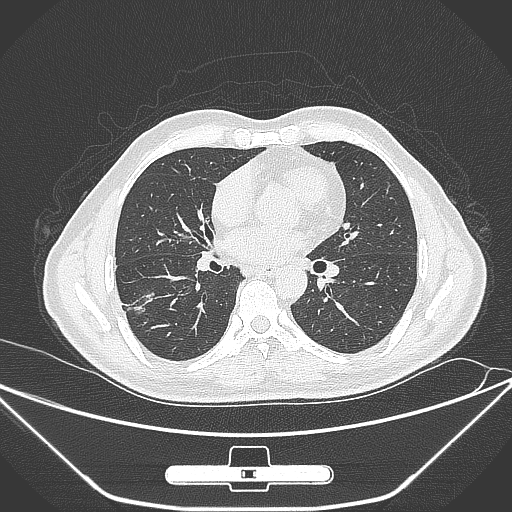
Chest CT, one axial slice. Slice 140 of 310 in the series (ordered by position). 120 kVp. Lung window (W 1500 / L -600 HU). 1 mm slice thickness. 512 × 512 image matrix, field of view 398 × 398 mm. Patient: male, 71 years. From the clinical record (not read from this slice): clinical TNM (as recorded): T1c N0 M0; histopathological grade: G2.
Outlined on this slice (bounding box drawn by a radiologist):
- lung tumour (recorded histology: adenocarcinoma): box from (x=116, y=286) to (x=158, y=327) px